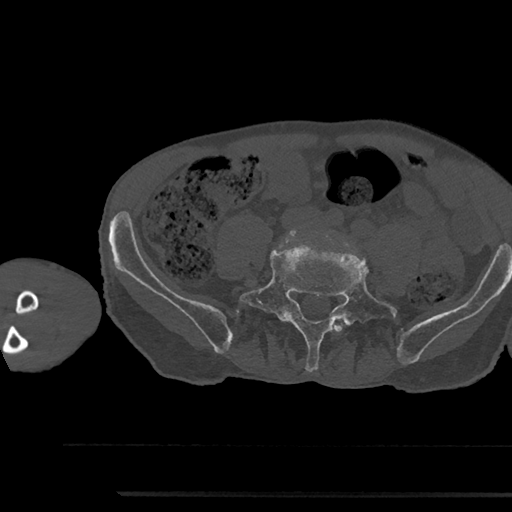
CT including the spine, one axial slice; position 357 of 797 along the scan axis; reconstruction kernel Br40s/3; bone window (W 1800 / L 400 HU); 0.5 mm slice thickness; 512 × 512 image matrix, field of view 367 × 367 mm. Patient: male, 79 years. From the clinical record (not read from this slice): primary cancer: prostate.
Structures marked on this image (semi-automatic segmentation, software-assisted and operator-edited):
- L4 vertebra: bounding box <333,323,343,333> (left, top, right, bottom; pixels)
- L5 vertebra: <240,248,400,372>